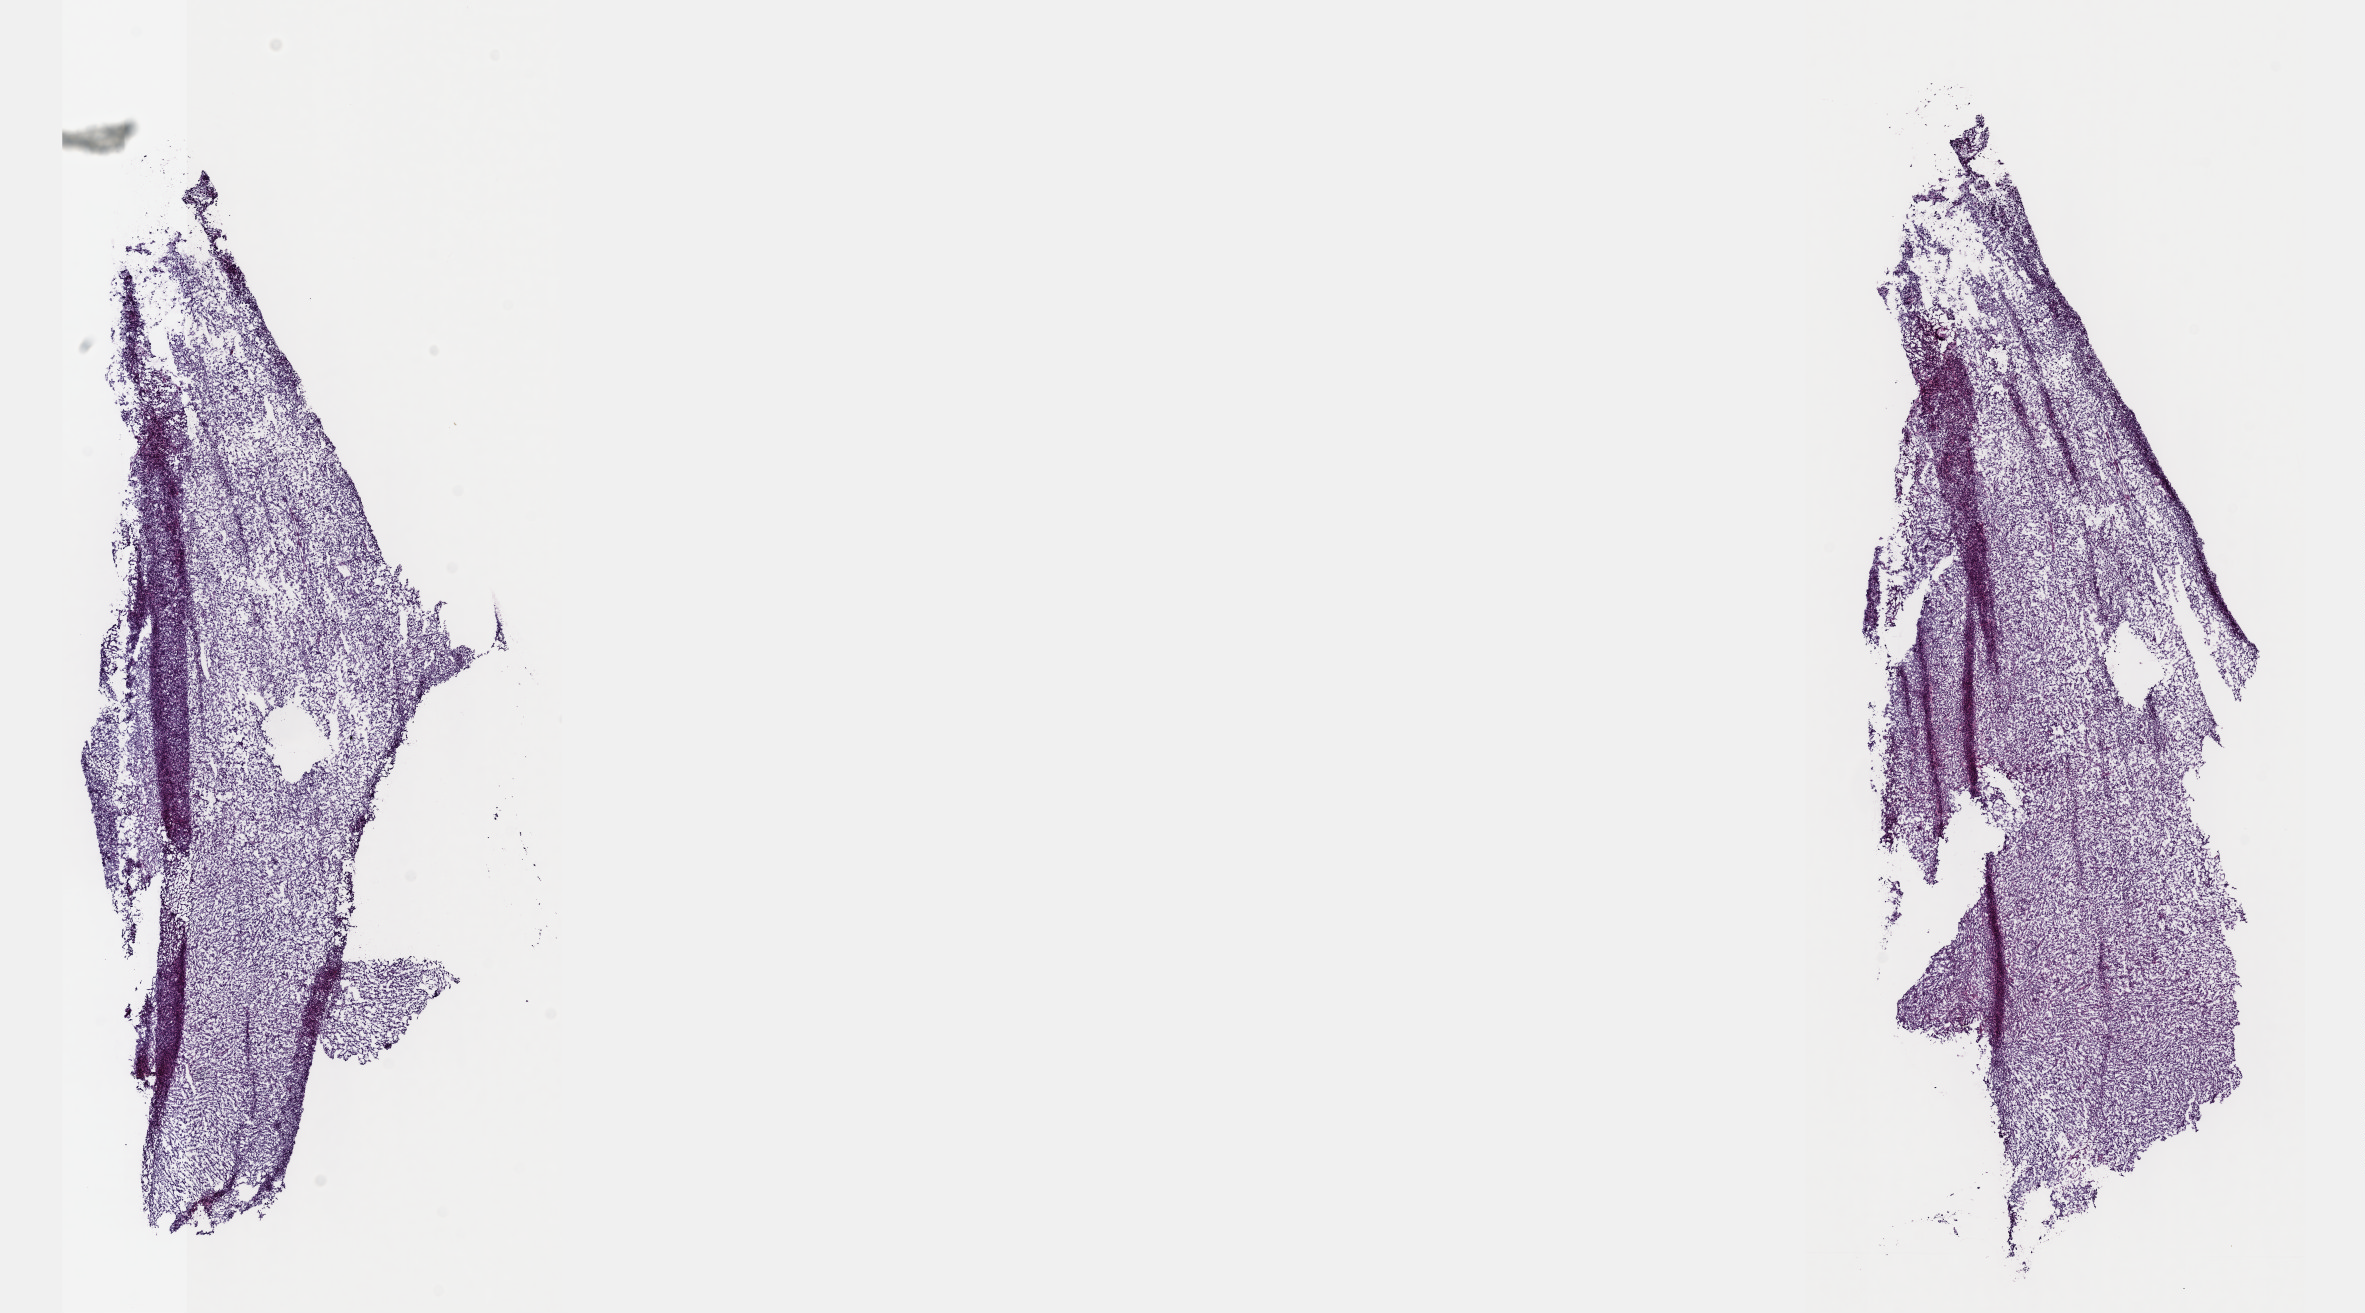
Whole-slide histology image, Hematoxylin and eosin (H&E) stained, shown as a low-resolution overview of the whole scanned area (about 19.1 x 10.6 mm); frozen section; sample: primary tumour, bladder. Patient: male, age at initial diagnosis 81 years. Histologic grade: high grade. Composition of this section per pathologist review: tumour cells 90%, tumour nuclei 90%, normal cells 0%, stromal cells 10%, necrosis 0%. Inflammatory infiltration, as recorded: lymphocyte infiltration 2%, monocyte infiltration 1%, neutrophil infiltration 3%.
Diagnosis: Papillary transitional cell carcinoma. TNM: T2a N0 MX. AJCC pathologic stage: II (6th edition). Lymph nodes positive (case pathology): 0 of 111 examined.